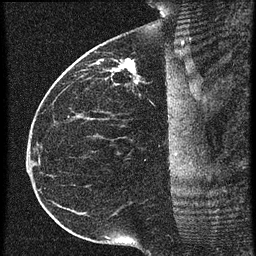
Breast MRI (dynamic contrast-enhanced), one sagittal slice; position 33 of 60 along the scan axis; 3 images stored at this slice position (order not interpretable as contrast timing); 1.5 T; TE 4.2 ms, TR 20.4 ms; 1.5 mm slice thickness; 256 × 256 image matrix. Female patient, age 35 years. From the clinical record (not read from this slice): setting: breast cancer imaged before/during neoadjuvant chemotherapy; receptor status: HR-positive, HER2-negative.
Structures marked on this image (semi-automatic segmentation, software-assisted and operator-edited):
- analysis volume of interest (the breast-tissue region the enhancement analysis was run in; not a lesion): bounding box [x1, y1, x2, y2] px = [84, 50, 179, 97]
- tumour enhancement mask (voxels above the 90 % enhancement threshold inside the analysis volume of interest): [98, 60, 137, 73]